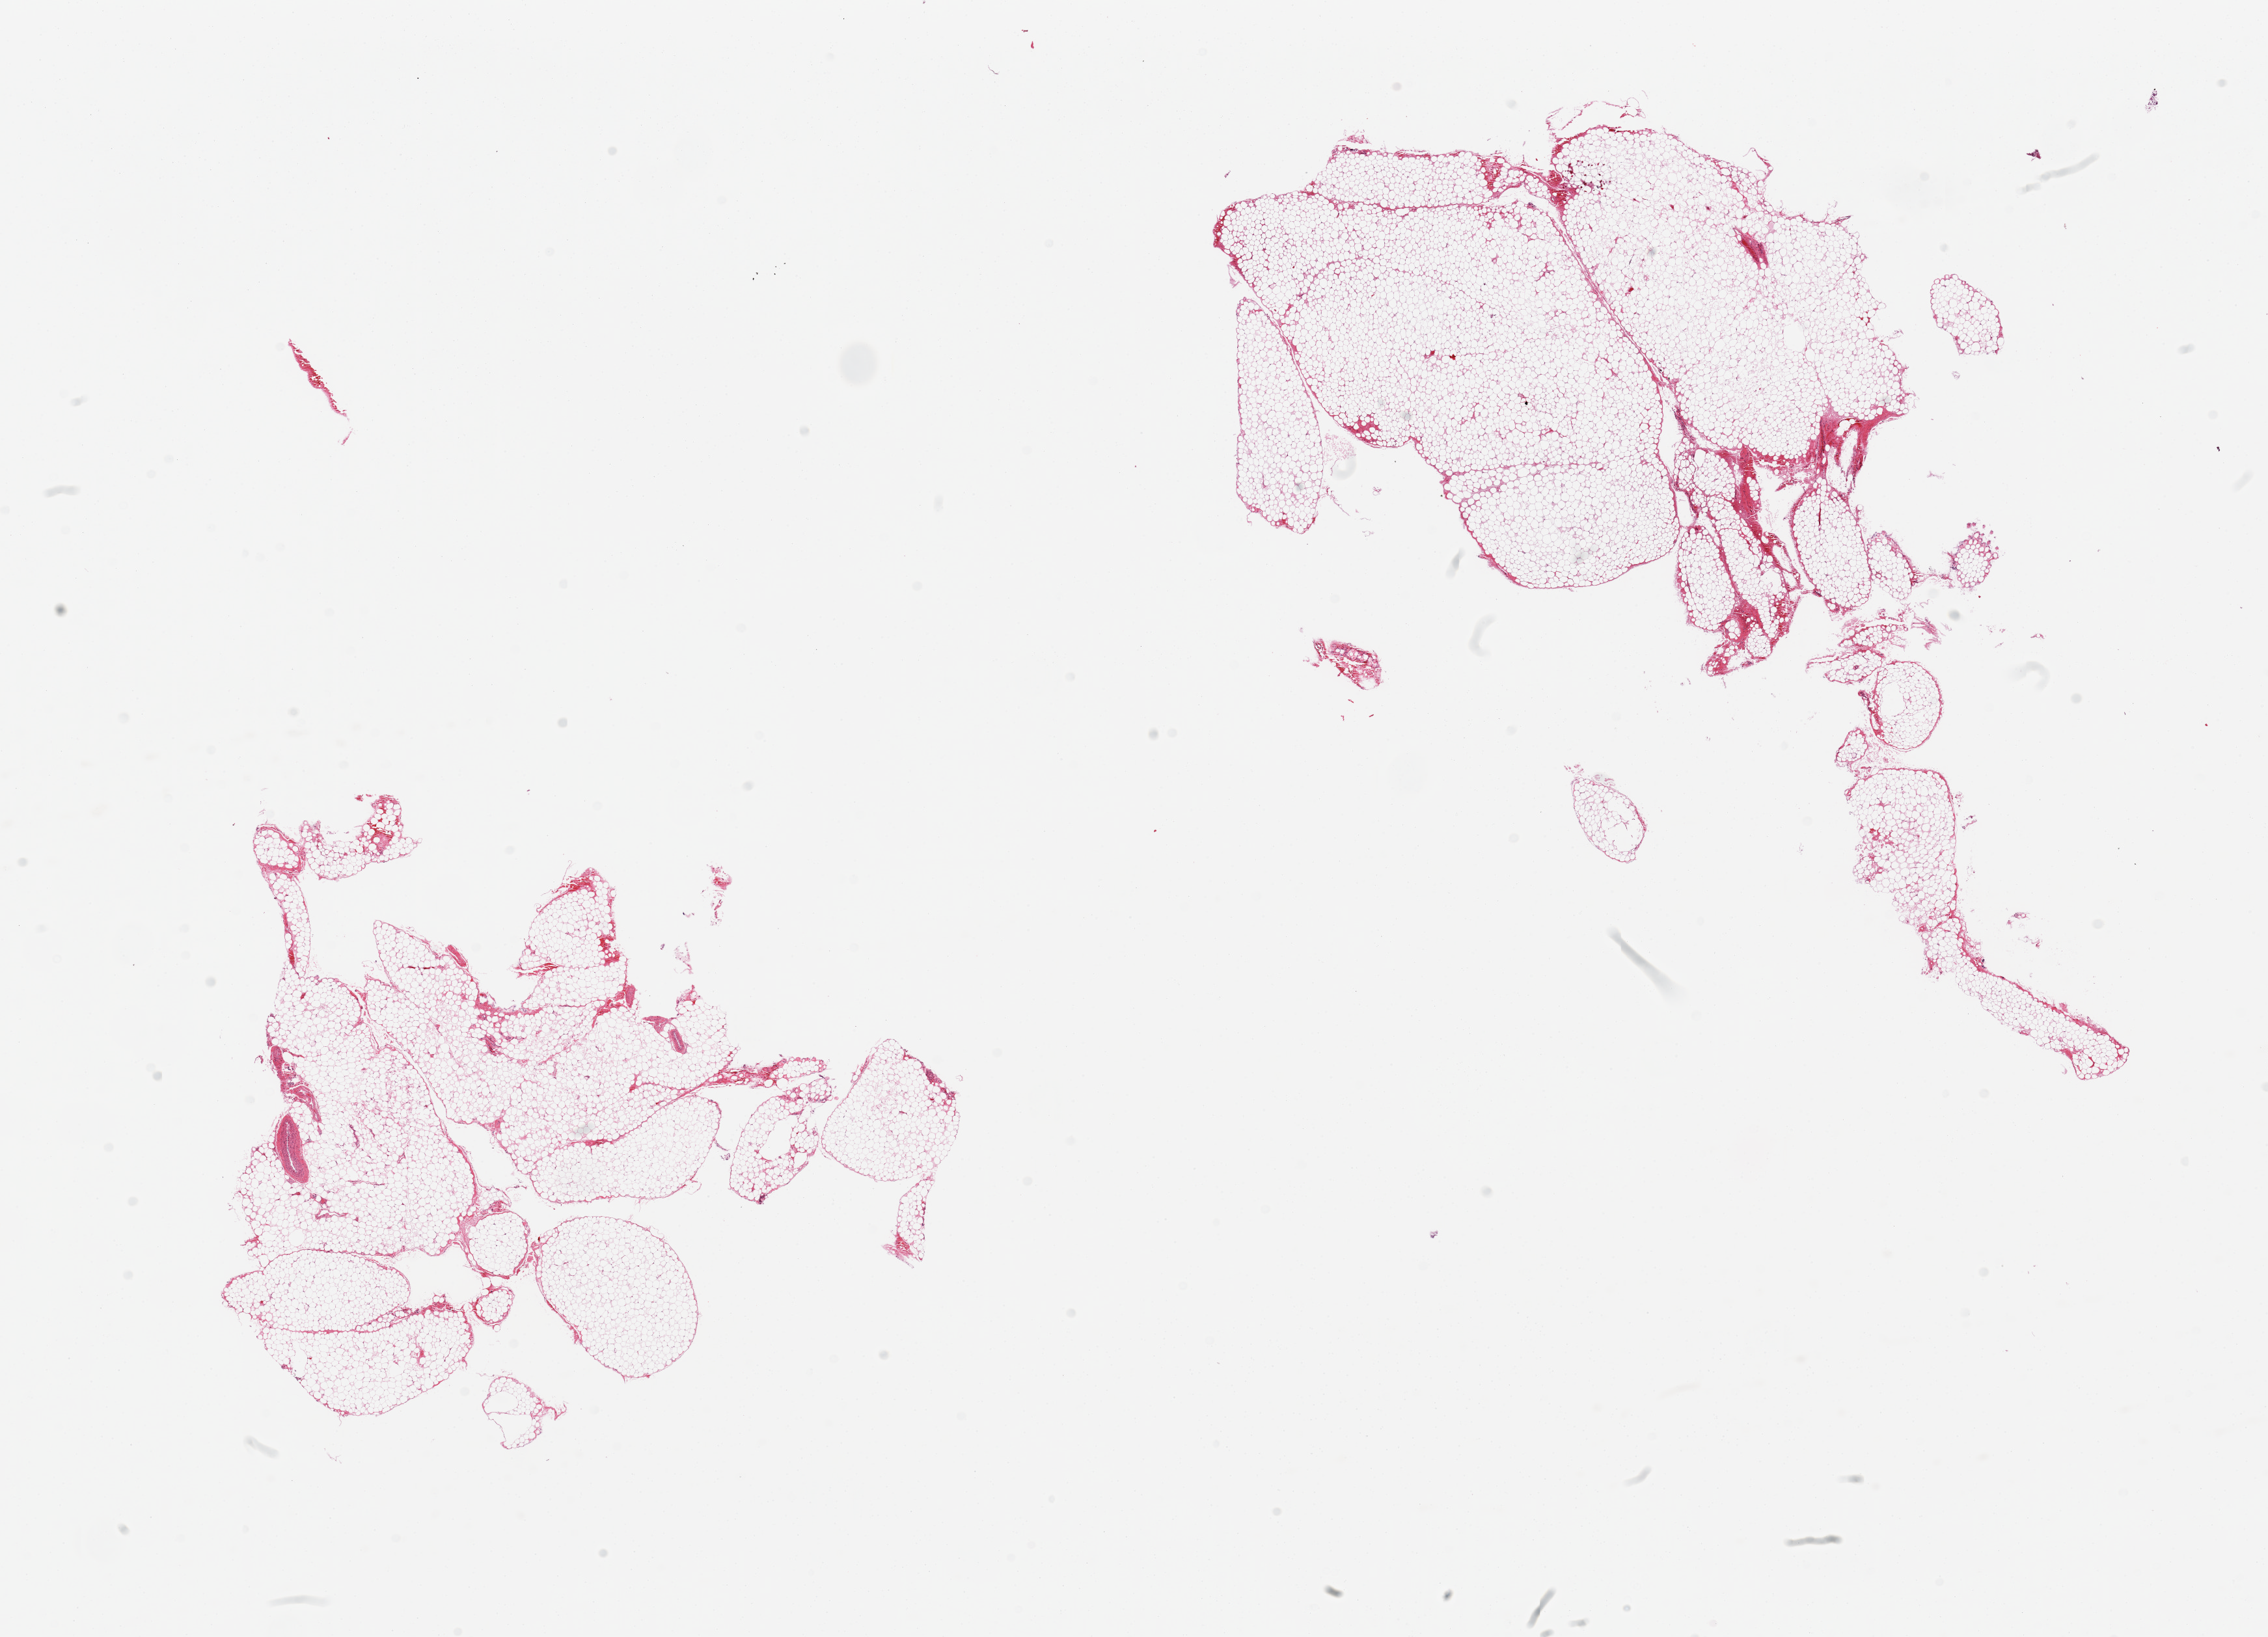
Hematoxylin and eosin (H&E) whole-slide image — low-resolution overview of the scanned area, about 27.6 x 19.9 mm, PAXgene-fixed paraffin-embedded (PFPE) section, section of omentum (target tissue), tissue donor sample. Female donor.
Review note (as recorded): 2 pieces.